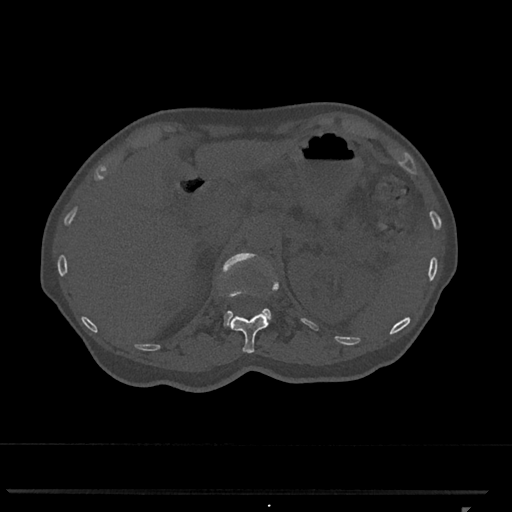
CT including the spine, one axial slice; position 440 of 793 along the scan axis; 120 kVp; bone window (W 1800 / L 400 HU); 0.5 mm slice thickness; 512 × 512 image matrix. Patient: female, 62 years. From the clinical record (not read from this slice): primary cancer: renal.
Structures marked on this image (semi-automatic segmentation, software-assisted and operator-edited):
- L1 vertebra: bounding box [x1, y1, x2, y2] px = [220, 252, 272, 327]
- T12 vertebra: [229, 254, 279, 353]